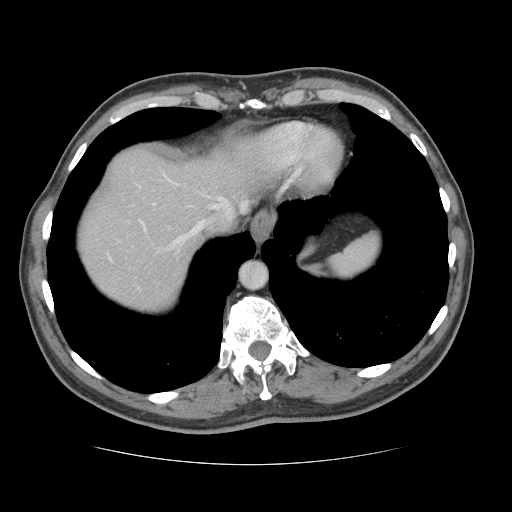
Contrast-enhanced abdominal CT, one axial slice; slice 113 of 134 in the series (ordered by position); reconstruction kernel STANDARD; soft-tissue window (W 400 / L 40 HU); 2.5 mm slice thickness; 512 × 512 image matrix, field of view 377 × 377 mm. Male patient, age 68 years. From the clinical record (not read from this slice): diagnosis: colorectal cancer liver metastases, imaged before liver resection; multiple liver metastases: yes; largest metastasis: 2.2 cm; disease in both lobes: no.
Annotated regions visible in this slice (manually delineated by an expert):
- hepatic veins: bounding box [x1, y1, x2, y2] px = [109, 171, 247, 258]
- liver: [79, 149, 246, 308]
- planned liver remnant (the part of the liver to remain after resection): [79, 149, 247, 302]